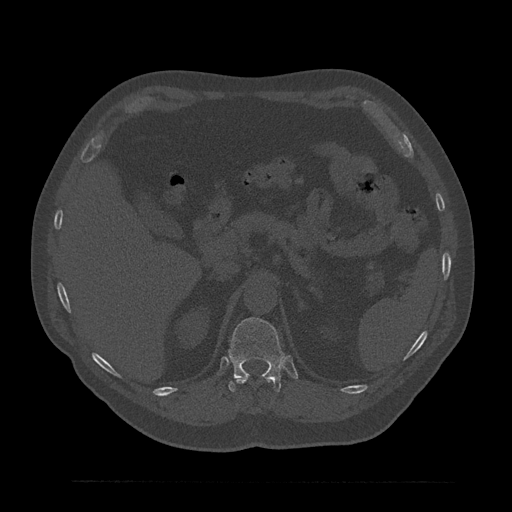
CT including the spine, one axial slice. Bone window (W 1800 / L 400 HU). 0.5 mm slice thickness. 512 × 512 image matrix. Patient: male, 61 years. From the clinical record (not read from this slice): primary cancer: prostate.
Annotated regions visible in this slice (semi-automatically segmented with operator editing):
- T11 vertebra: bounding box (x1, y1, x2, y2) in pixels: (236, 378, 272, 384)
- T12 vertebra: (228, 317, 285, 392)